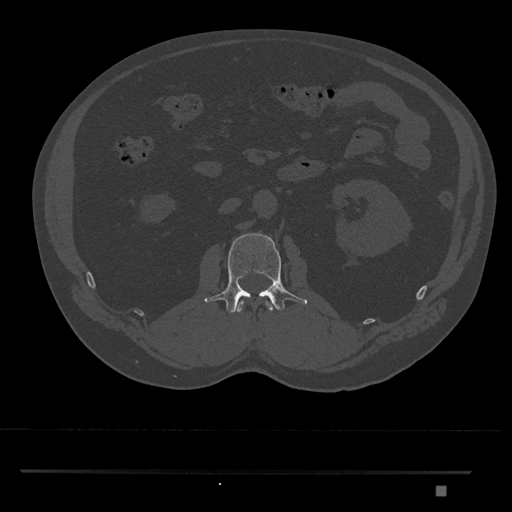
CT including the spine, one axial slice; position 763 of 1134 along the scan axis; bone window (W 1800 / L 400 HU); 0.5 mm slice thickness; 512 × 512 image matrix, field of view 429 × 429 mm. Patient: male, 65 years. Case-level facts recorded for this patient, not image findings: primary cancer: prostate.
Structures marked on this image (semi-automatically segmented with operator editing):
- L1 vertebra: bounding box <235,300,273,313> (left, top, right, bottom; pixels)
- L2 vertebra: <204,233,308,313>